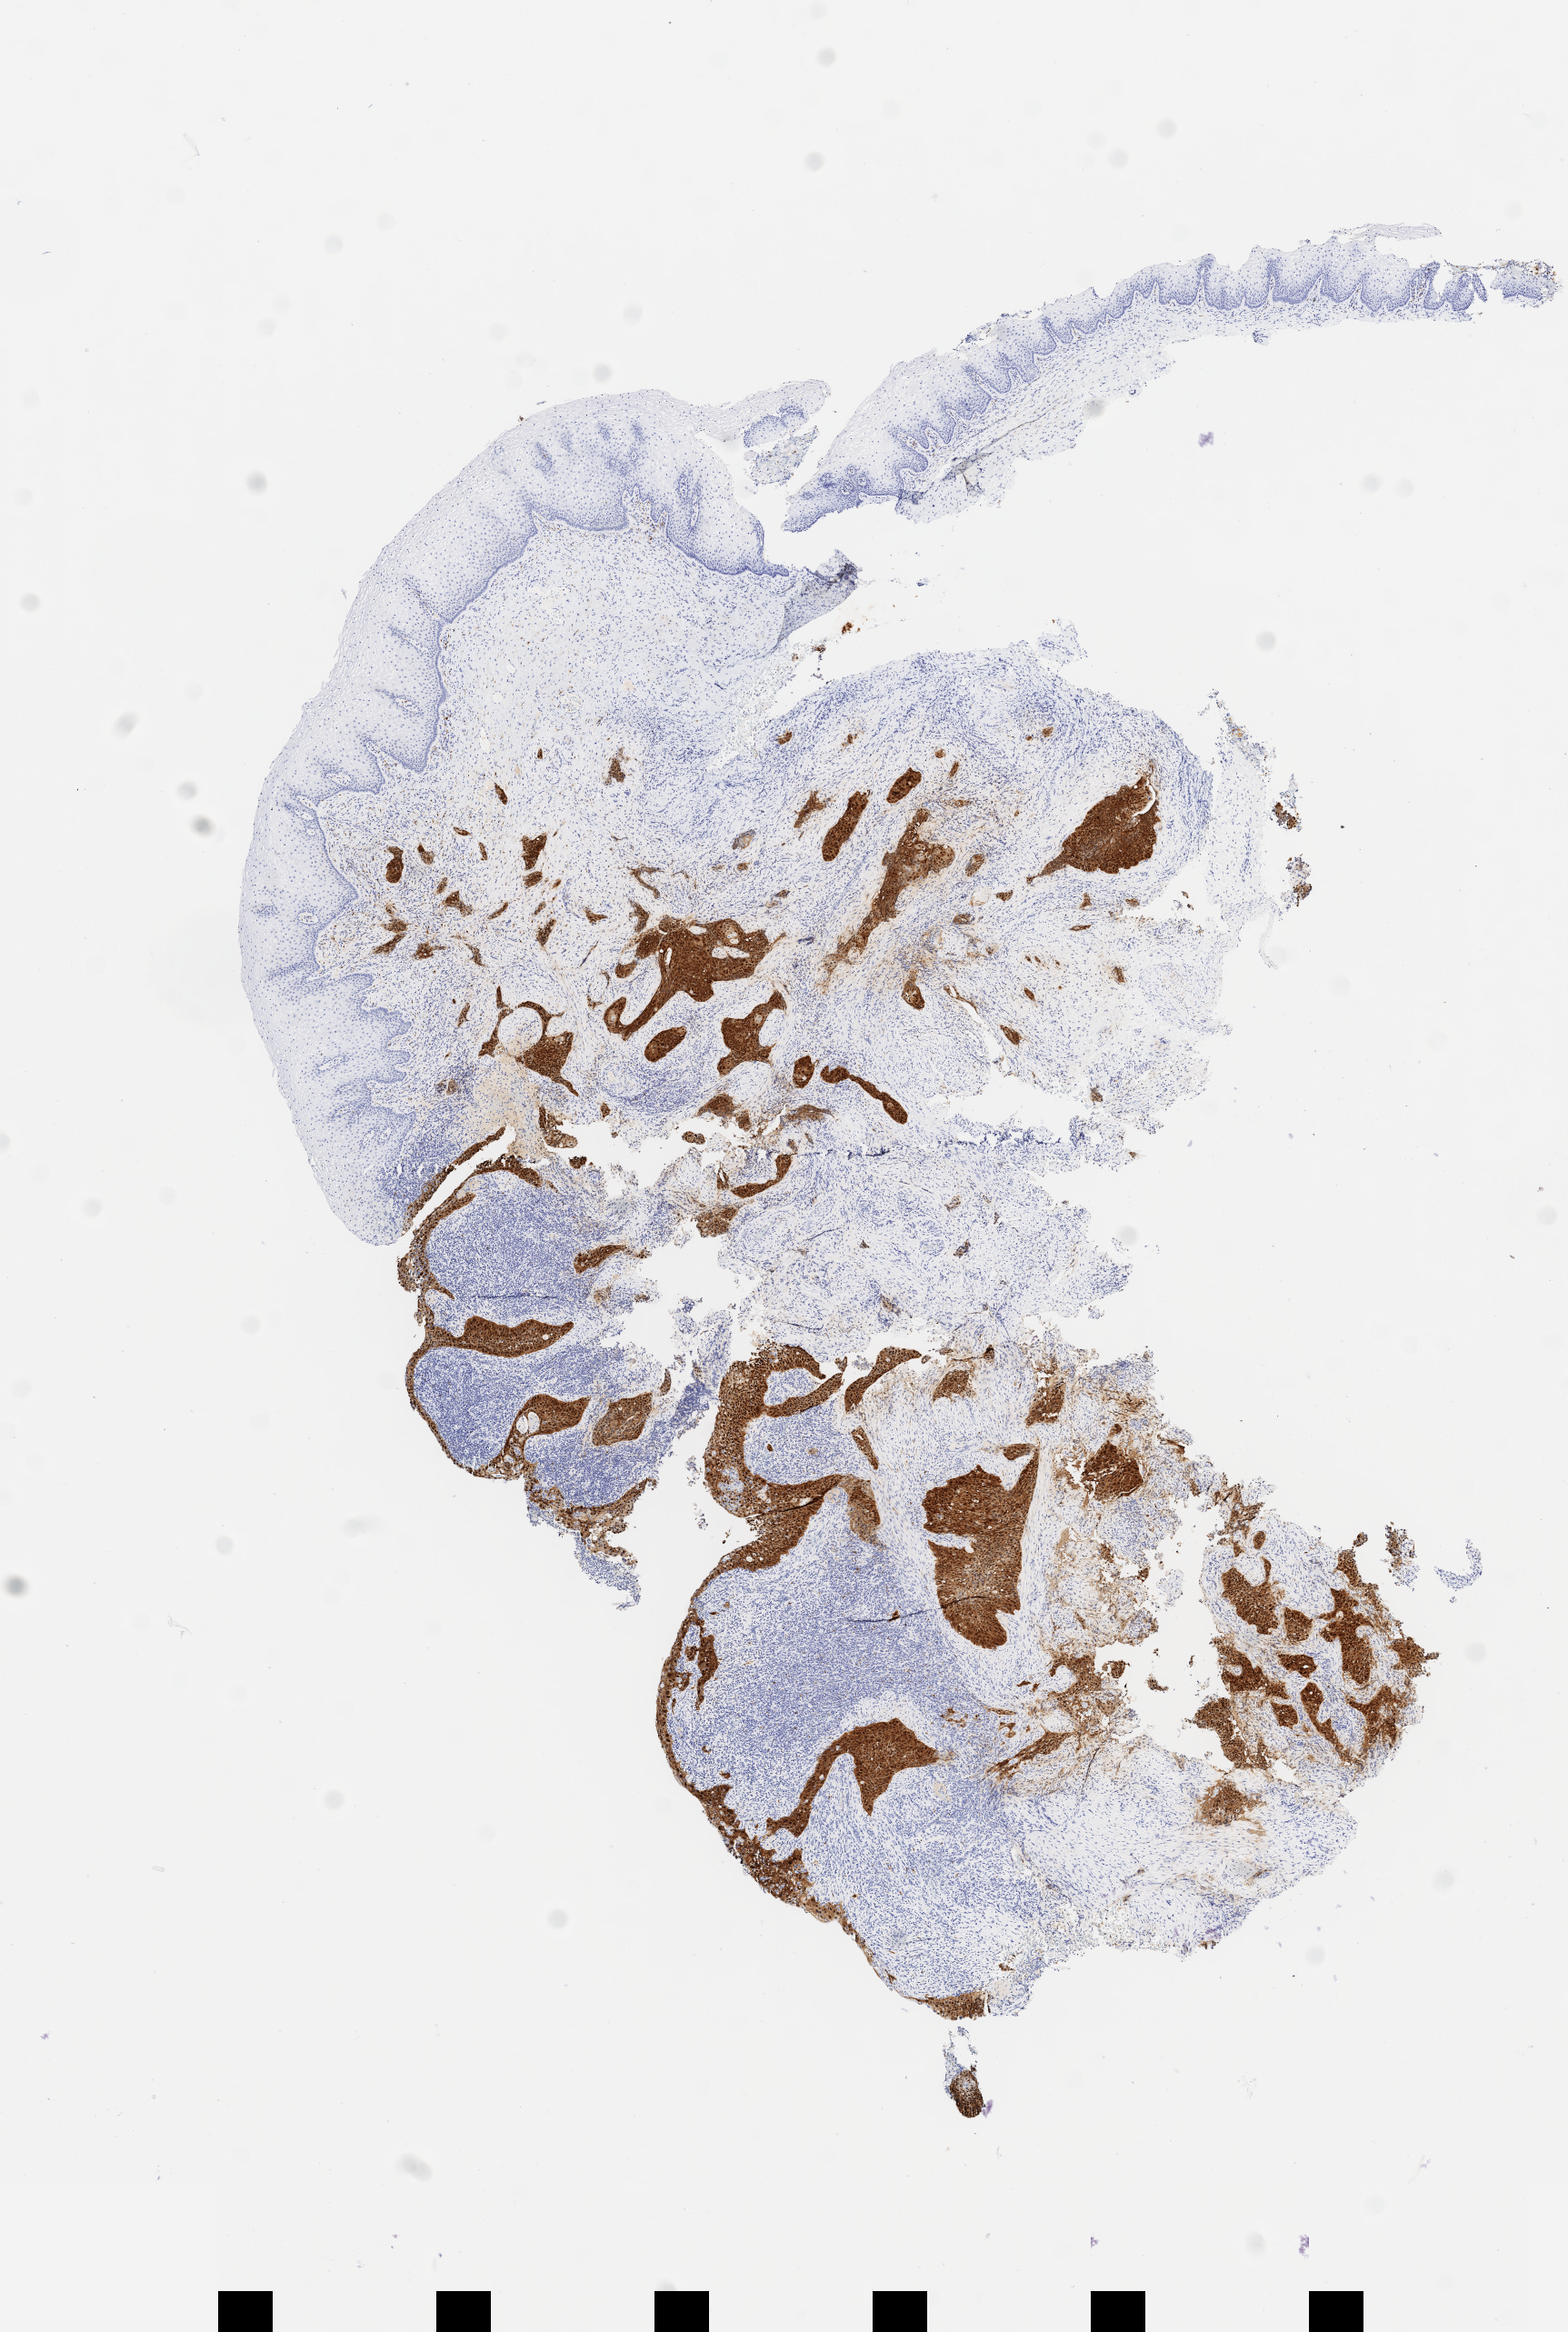
IHC for p16 (p16INK4a), whole-slide image, whole scanned area (about 6.9 x 10.2 mm) shown as a low-resolution overview. Specimen: tumor tissue. Anatomic site: cervix. Patient female; aged 39.
Histologic diagnosis: Squamous cell carcinoma, large cell, nonkeratinizing, NOS.